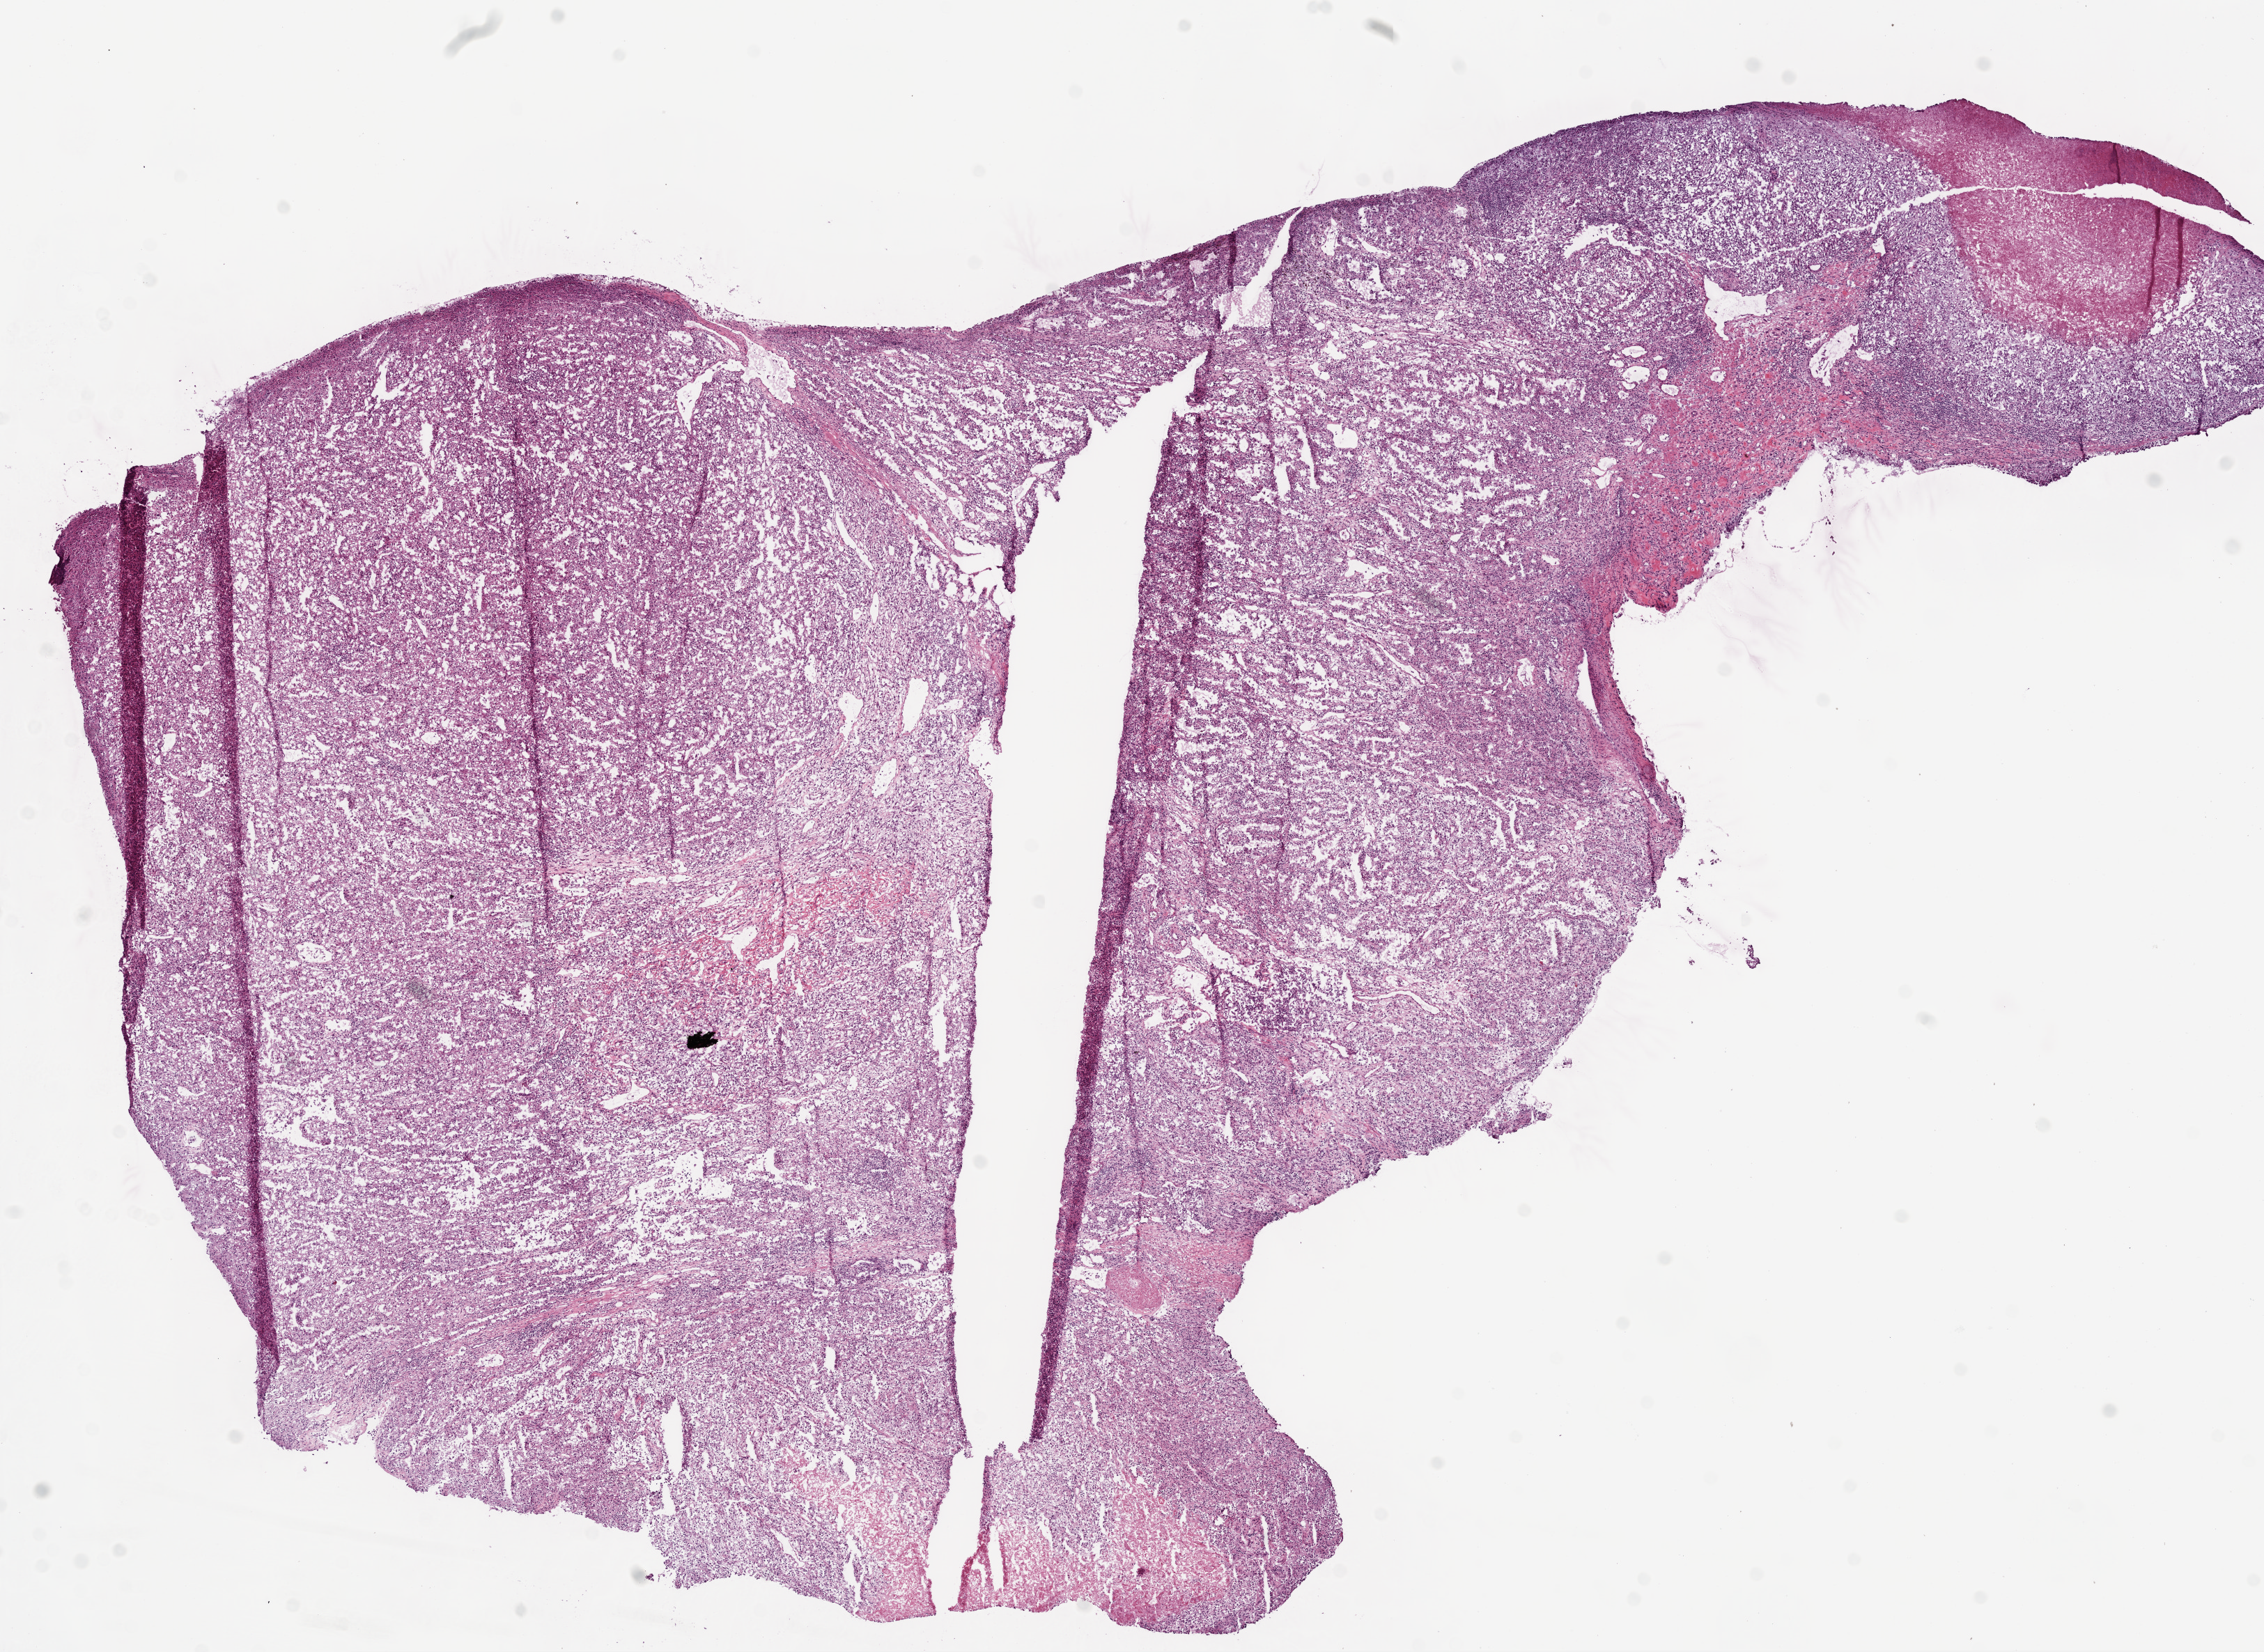
H&E whole-slide image, whole scanned area (about 13.0 x 9.5 mm) shown as a low-resolution overview. Frozen section. Sample: primary tumour, kidney. Patient: male, age at initial diagnosis 62 years. Histologic grade: G4 (undifferentiated). Composition of this section per pathologist review: tumour cells 95%, tumour nuclei 90%, necrosis 5%. Inflammatory infiltration, as recorded: lymphocyte infiltration 5%.
AJCC pathologic stage: IV. Lymph nodes positive (case pathology): 0 of 5 examined. Histologic diagnosis: Clear cell adenocarcinoma, NOS. Laterality: right.